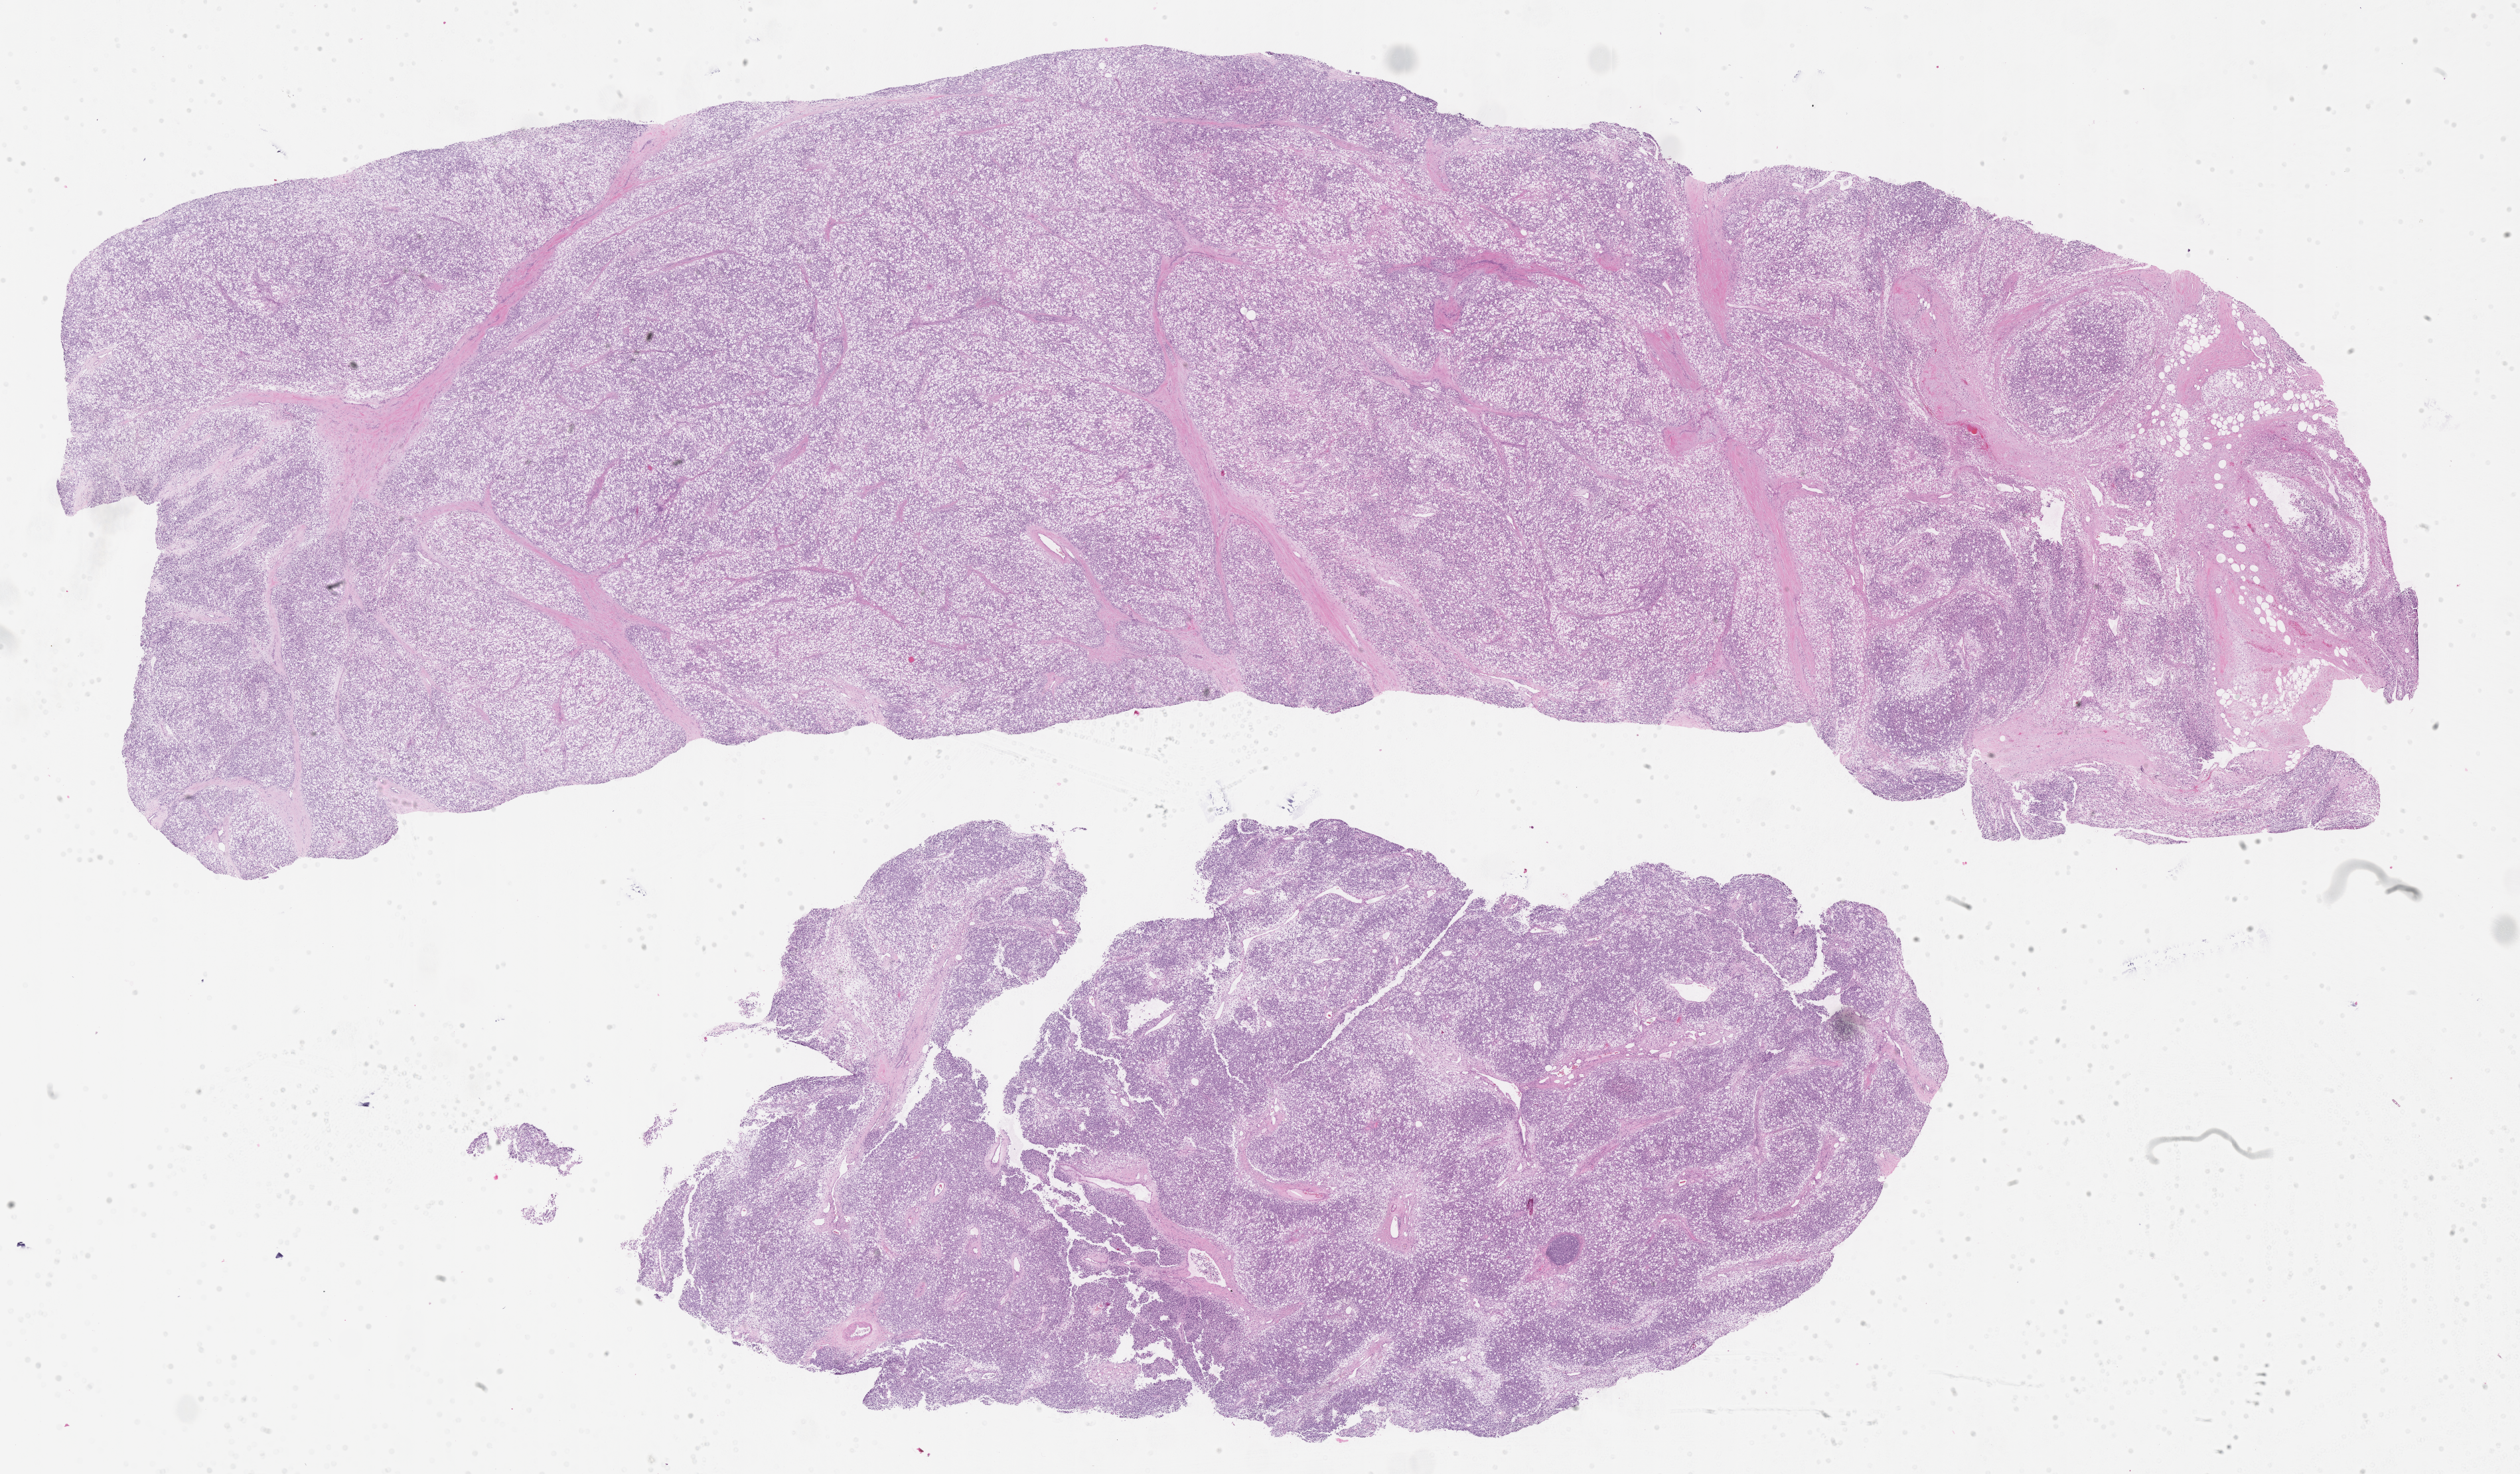
Haematoxylin and eosin whole-slide image of tumor tissue — whole scanned area (about 30.7 x 18.0 mm) shown as a low-resolution overview, formalin-fixed, paraffin-embedded (FFPE) tissue, site: abdomen (Bladder). Female patient, age at diagnosis 6.9 years.
Diagnosis: rhabdomyosarcoma; histological classification: embryonal rhabdomyosarcoma.